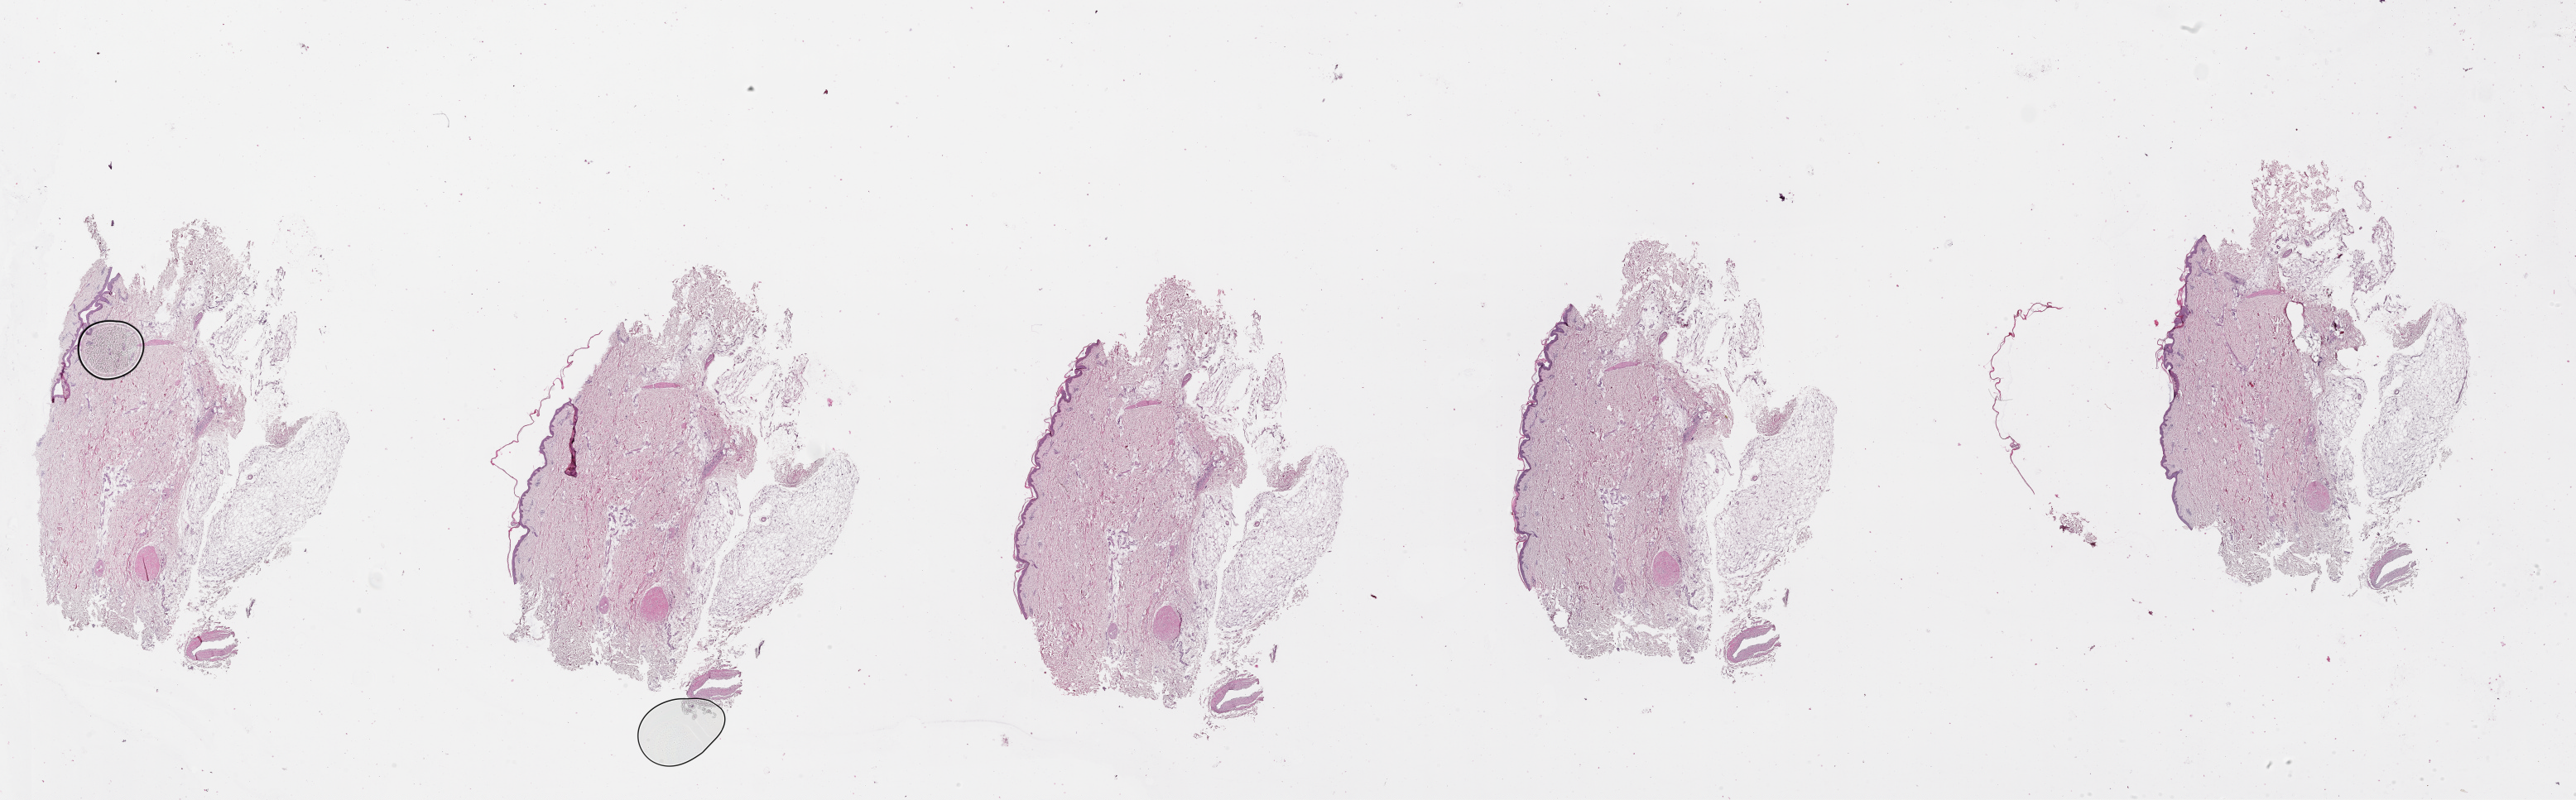
Whole-slide histology image, H&E, low-resolution overview of the scanned area, about 50.1 x 15.6 mm. Female, 70 y/o.
• patient diagnosis: Malignant melanoma, NOS